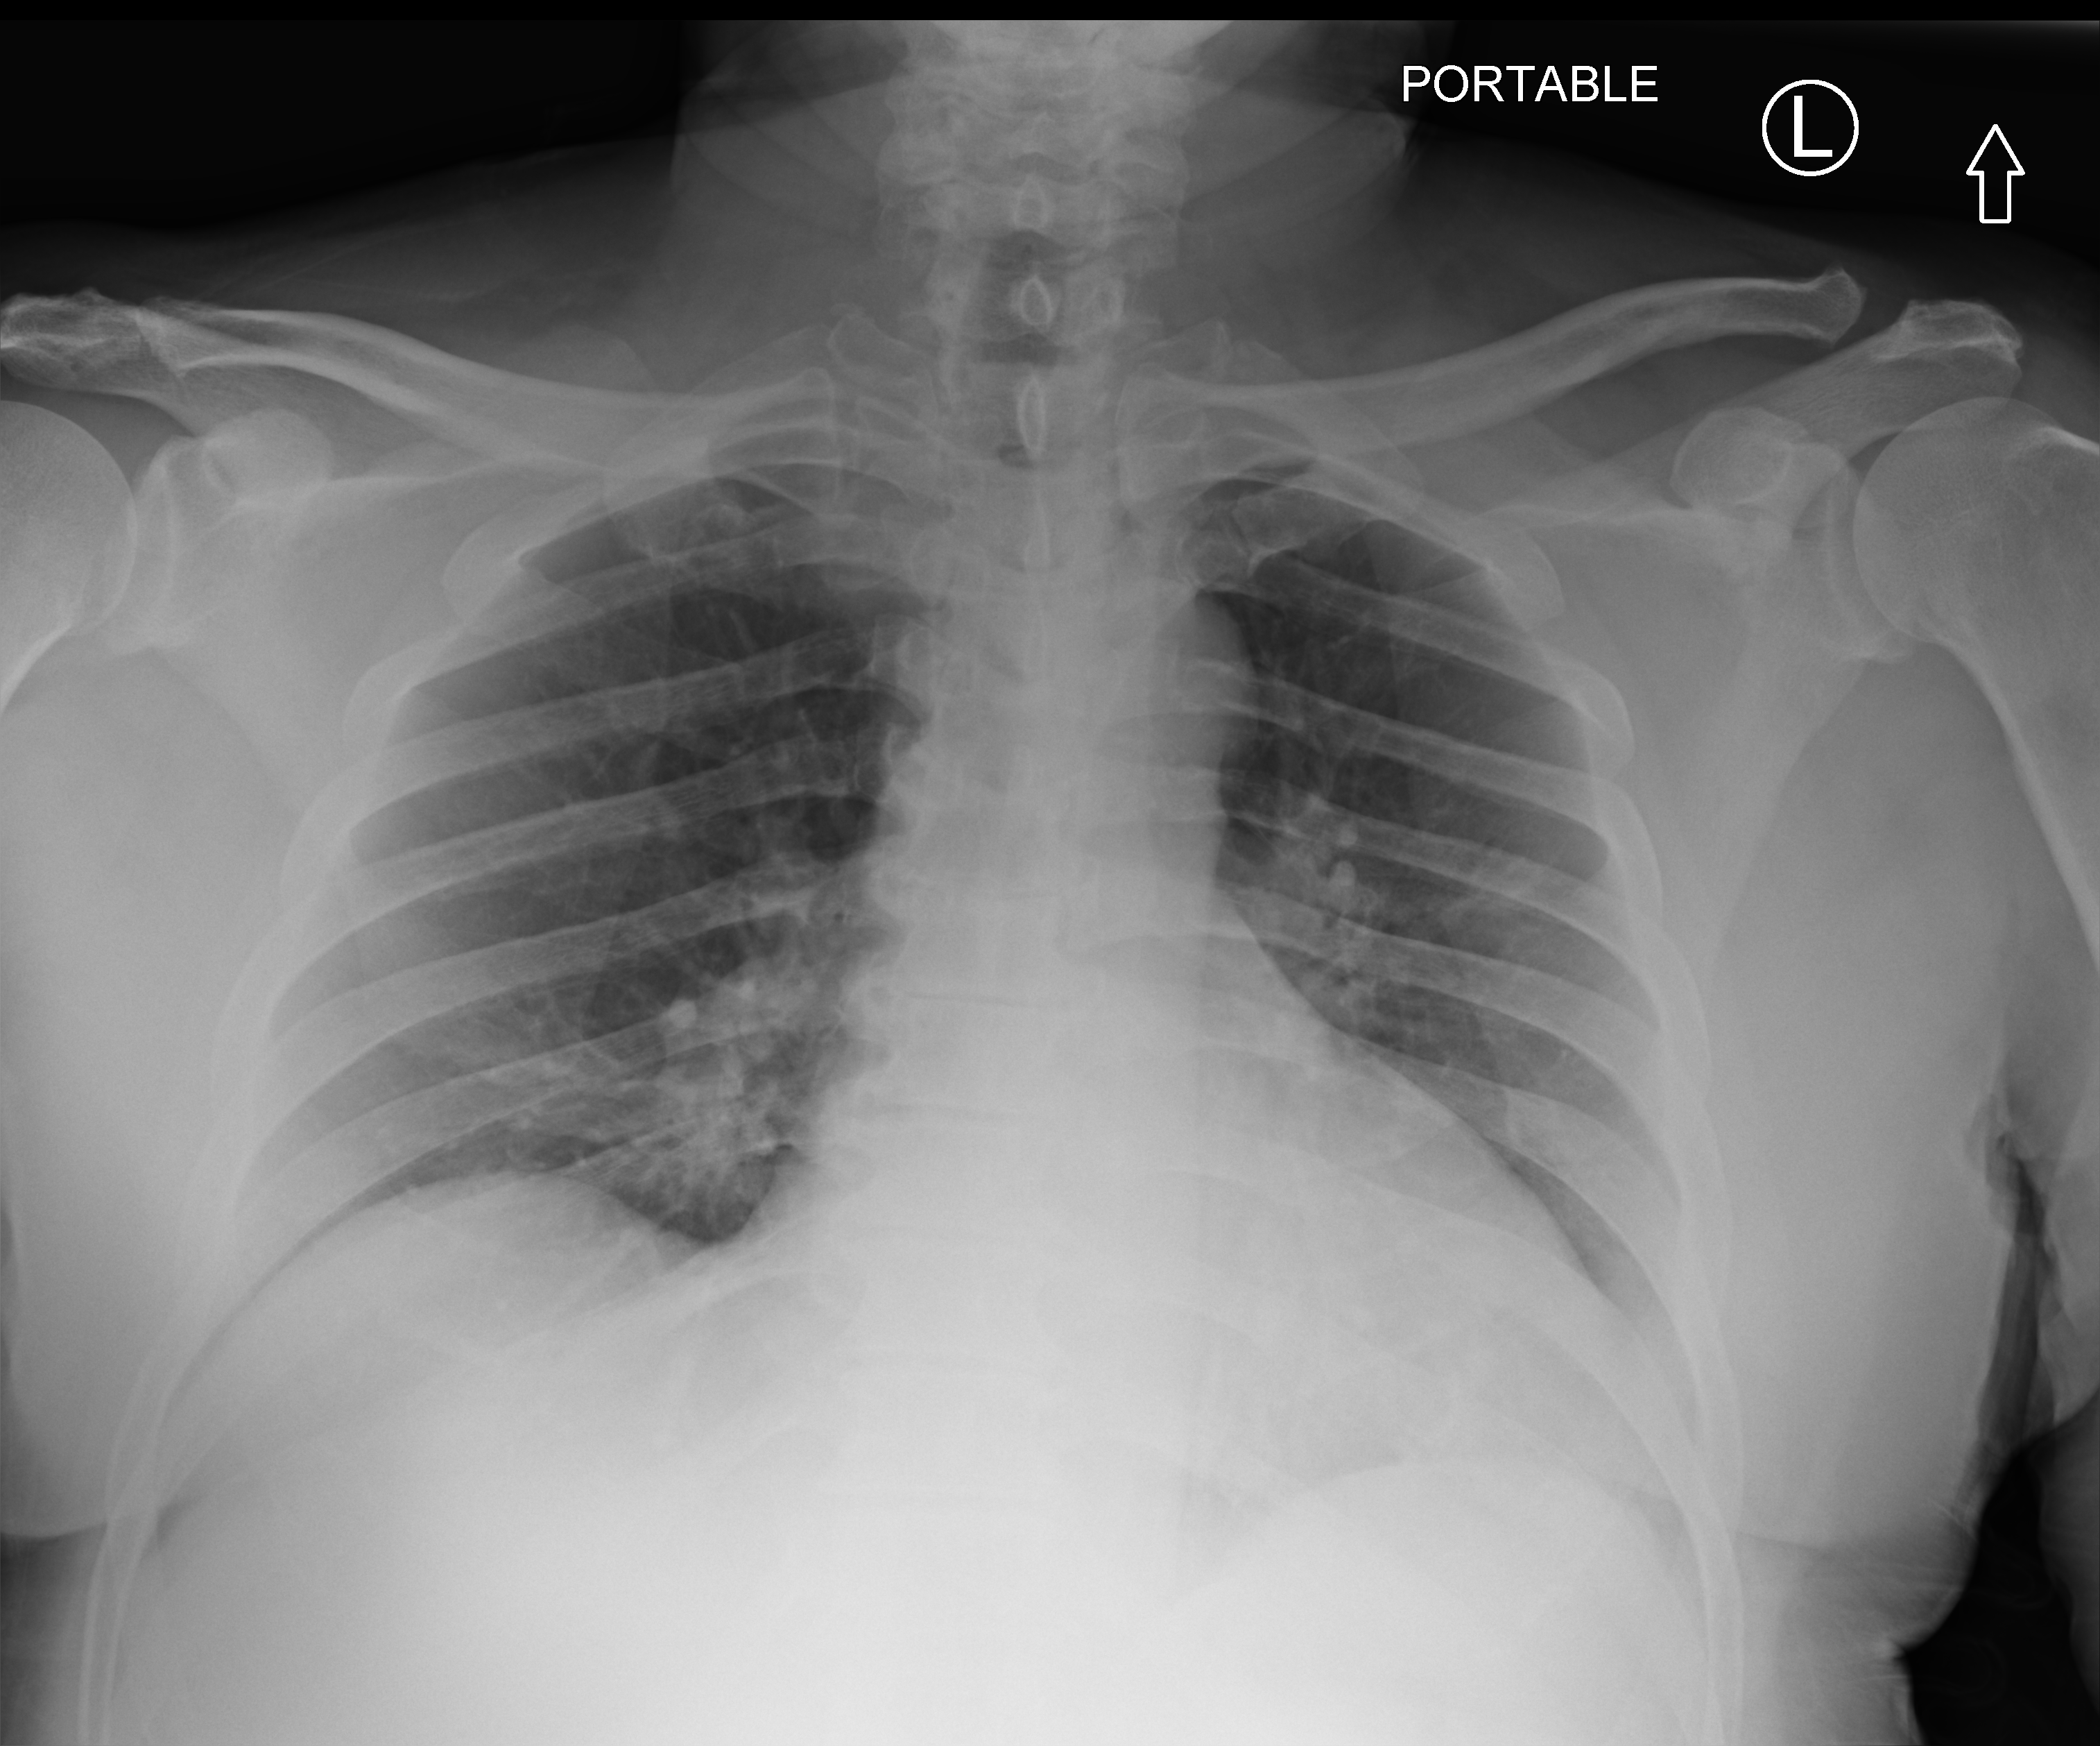
Portable chest radiograph, anteroposterior (AP) projection. Patient hospitalised with COVID-19; male, aged 60–74 years.
From the hospital-stay record, not from the radiograph (when in the stay this image was taken is not recorded):
- length of hospital stay: 6 days
- hypertension (admission record): yes